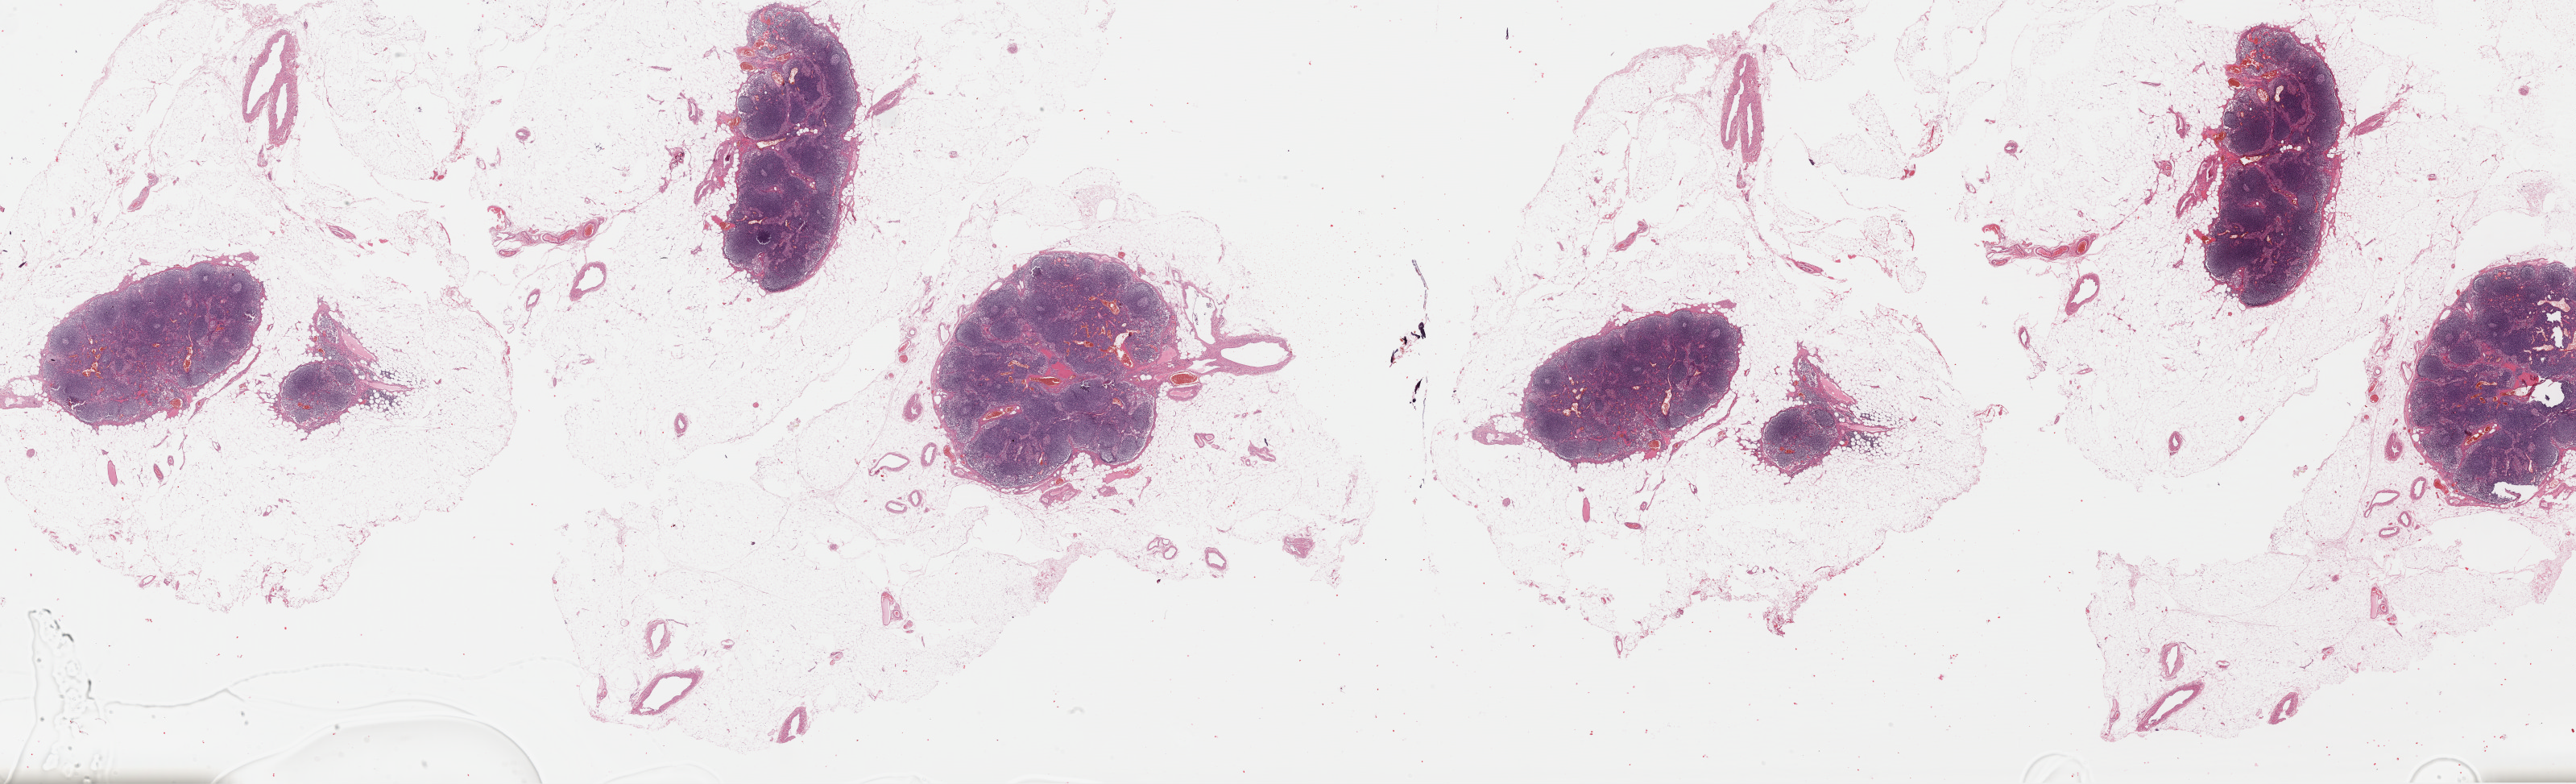
Digitized Hematoxylin and eosin (H&E) stained tissue section (whole slide), low-resolution overview of the scanned area, about 50.3 x 15.3 mm, FFPE section, metastatic tumour sample, sampled site: lymph node. Patient: male, age at initial diagnosis 65 years.
This section: metastatic tumour tissue. Patient diagnosis: Malignant melanoma, NOS.